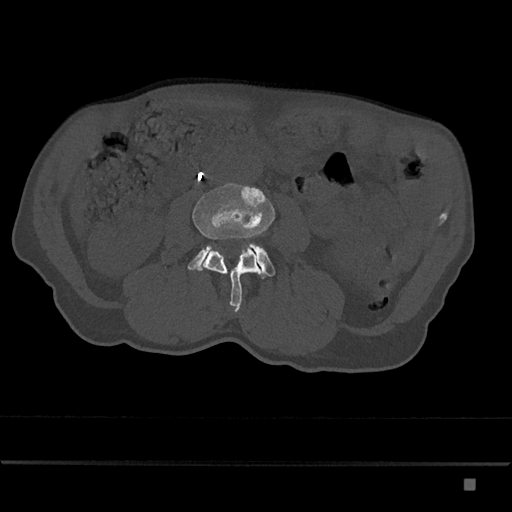
CT including the spine, one axial slice; slice 382 of 797 in the series (ordered by position); reconstruction kernel Br40s/3; bone window (W 1800 / L 400 HU); 0.5 mm slice thickness; 512 × 512 image matrix. Patient: male, 72 years. Case-level facts recorded for this patient, not image findings: primary cancer: prostate.
Annotated regions visible in this slice (semi-automatic segmentation, software-assisted and operator-edited):
- L3 vertebra: box from (x=192, y=183) to (x=275, y=312) px
- L4 vertebra: (x=188, y=243)–(x=275, y=279)